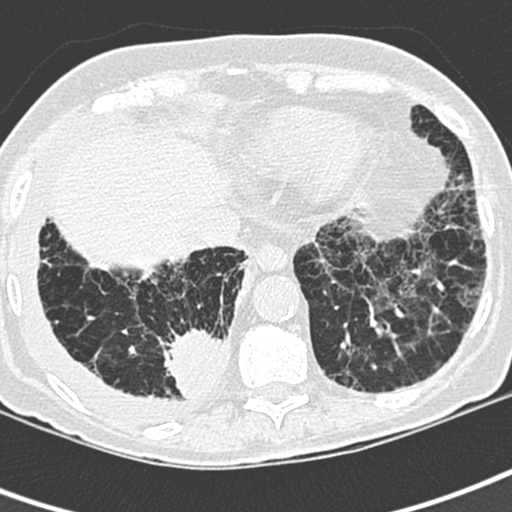
Low-dose screening chest CT, one axial slice. Position 72 of 220 along the scan axis. Lung window (W 1500 / L -600 HU). 512 × 512 image matrix.
Annotated regions visible in this slice (manually delineated by an expert):
- lesion 1 (tumor, lower lobe of right lung): box from (x=164, y=328) to (x=223, y=399) px